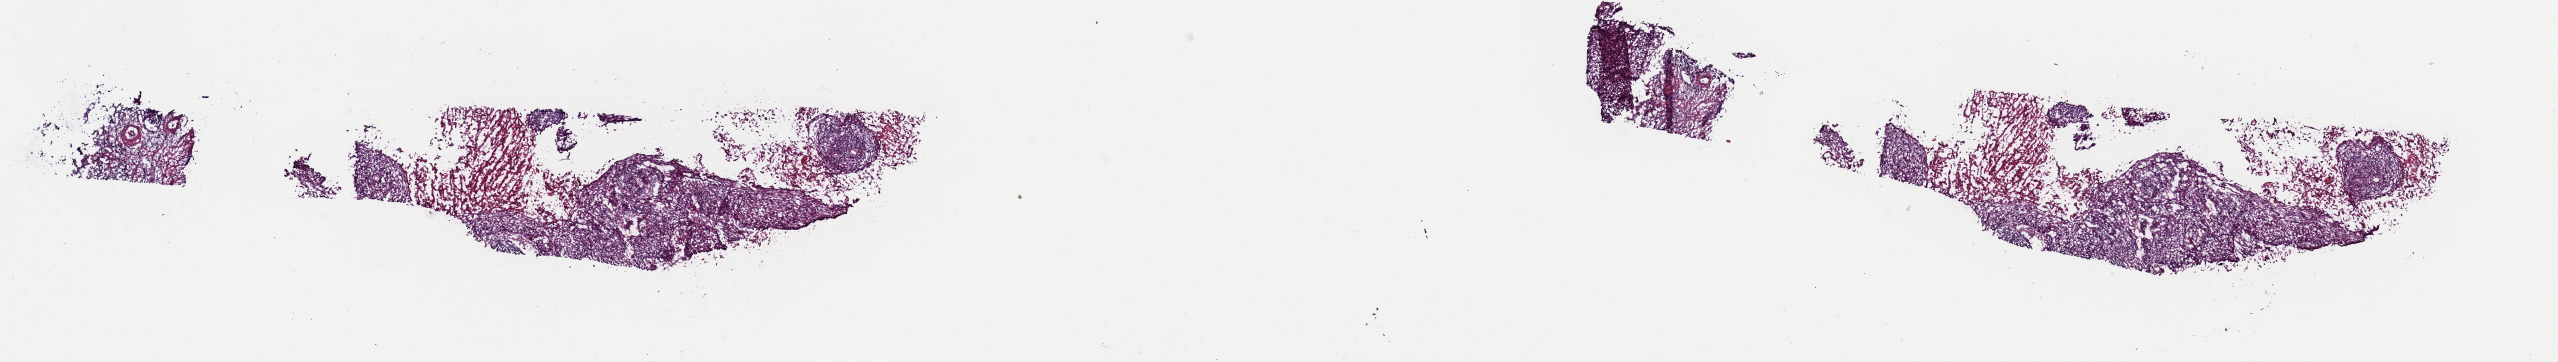
Whole-slide histology image, H&E — a low-resolution overview of the entire scanned area, about 20.2 x 2.9 mm (slide scanned at 40x). Frozen section from the top of the tissue portion. Cervix, primary tumour sample. Female, age 63 years at initial diagnosis. Histologic grade: G2 (moderately differentiated). Slide review estimates, as recorded: tumour cells 90%, tumour nuclei 80%, normal cells 0%, stromal cells 0%, necrosis 10%. Inflammatory infiltration, as recorded: lymphocyte infiltration 3%, monocyte infiltration 0%, neutrophil infiltration 0%.
FIGO stage: IB. Pathologic diagnosis: Squamous cell carcinoma, keratinizing, NOS (cervix uteri).